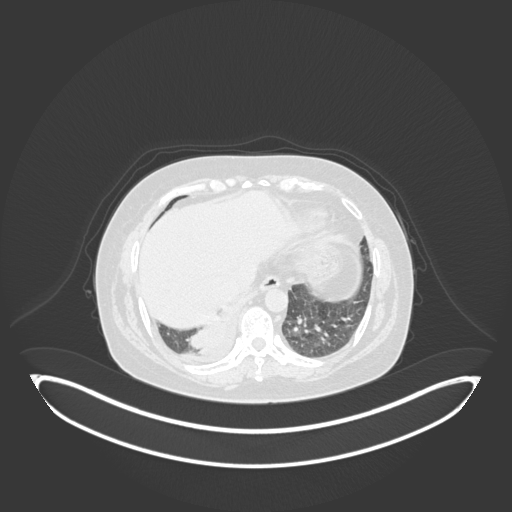
Chest CT, one axial slice. Slice 29 of 231 in the series (ordered by position). Lung window (W 1500 / L -600 HU). 1 mm slice thickness. 512 × 512 image matrix, field of view 500 × 500 mm. Female patient, age 56 years. Case-level facts recorded for this patient, not image findings: clinical TNM (as recorded): T2b N1 M0.
Structures marked on this image (rectangle marked by the reading radiologist):
- lung tumour (recorded histology: small cell carcinoma): box from (x=180, y=307) to (x=230, y=352) px